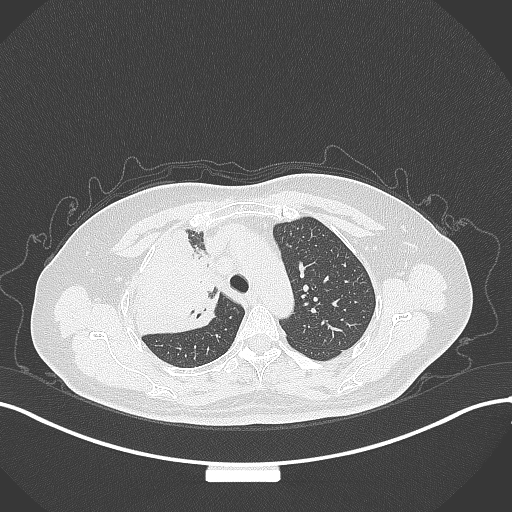
Chest CT, one axial slice; slice 234 of 309 in the series (ordered by position); reconstruction kernel B70f; lung window (W 1500 / L -600 HU); 1 mm slice thickness; 512 × 512 image matrix, field of view 400 × 400 mm. Female patient, age 60 years. From the clinical record (not read from this slice): clinical TNM (as recorded): T3 N1 M1.
Outlined on this slice (bounding box drawn by a radiologist):
- lung tumour (recorded histology: adenocarcinoma): bounding box [x1, y1, x2, y2] px = [123, 231, 225, 336]